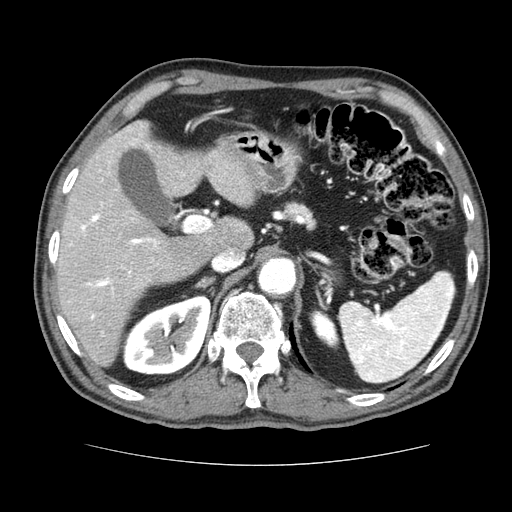
Contrast-enhanced abdominal CT (liver protocol), one axial slice. Slice 45 of 79 in the series (ordered by position). Reconstruction kernel STANDARD. 120 kVp. Soft-tissue window (W 400 / L 40 HU). 512 × 512 image matrix, field of view 360 × 360 mm. Case-level facts recorded for this patient, not image findings: diagnosis: hepatocellular carcinoma (patient treated with transarterial chemoembolisation; whether this scan precedes or follows treatment is not stated here); TNM stage (as recorded): Stage-I; Child-Pugh class: A; tumour nodularity: uninodular.
Structures marked on this image (semi-automatic segmentation, software-assisted and operator-edited):
- liver parenchyma outside the tumour (the mass and vessels are separate outlines, so this box may not span the whole liver): bounding box [x1, y1, x2, y2] px = [56, 120, 254, 365]
- liver vessels: [69, 128, 159, 337]